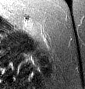
MRI of an extremity soft-tissue mass, one axial slice. Position 30 of 46 along the scan axis. T2-weighted fat-saturated. MR volume resampled by the dataset authors to the PET/CT grid (not the native acquisition matrix). 3.27 mm slice thickness. 85 × 89 image matrix, field of view 83 × 87 mm. Female patient. From the clinical record (not read from this slice): histological type: leiomyosarcoma; grade: intermediate; site of the primary tumour: parascapusular.
Outlined on this slice (expert contour drawn on MRI and transferred to this co-registered scan by the dataset authors):
- gross tumour volume including surrounding oedema: bounding box [x1, y1, x2, y2] px = [24, 23, 41, 38]
- gross tumour volume (mass): [25, 23, 37, 36]